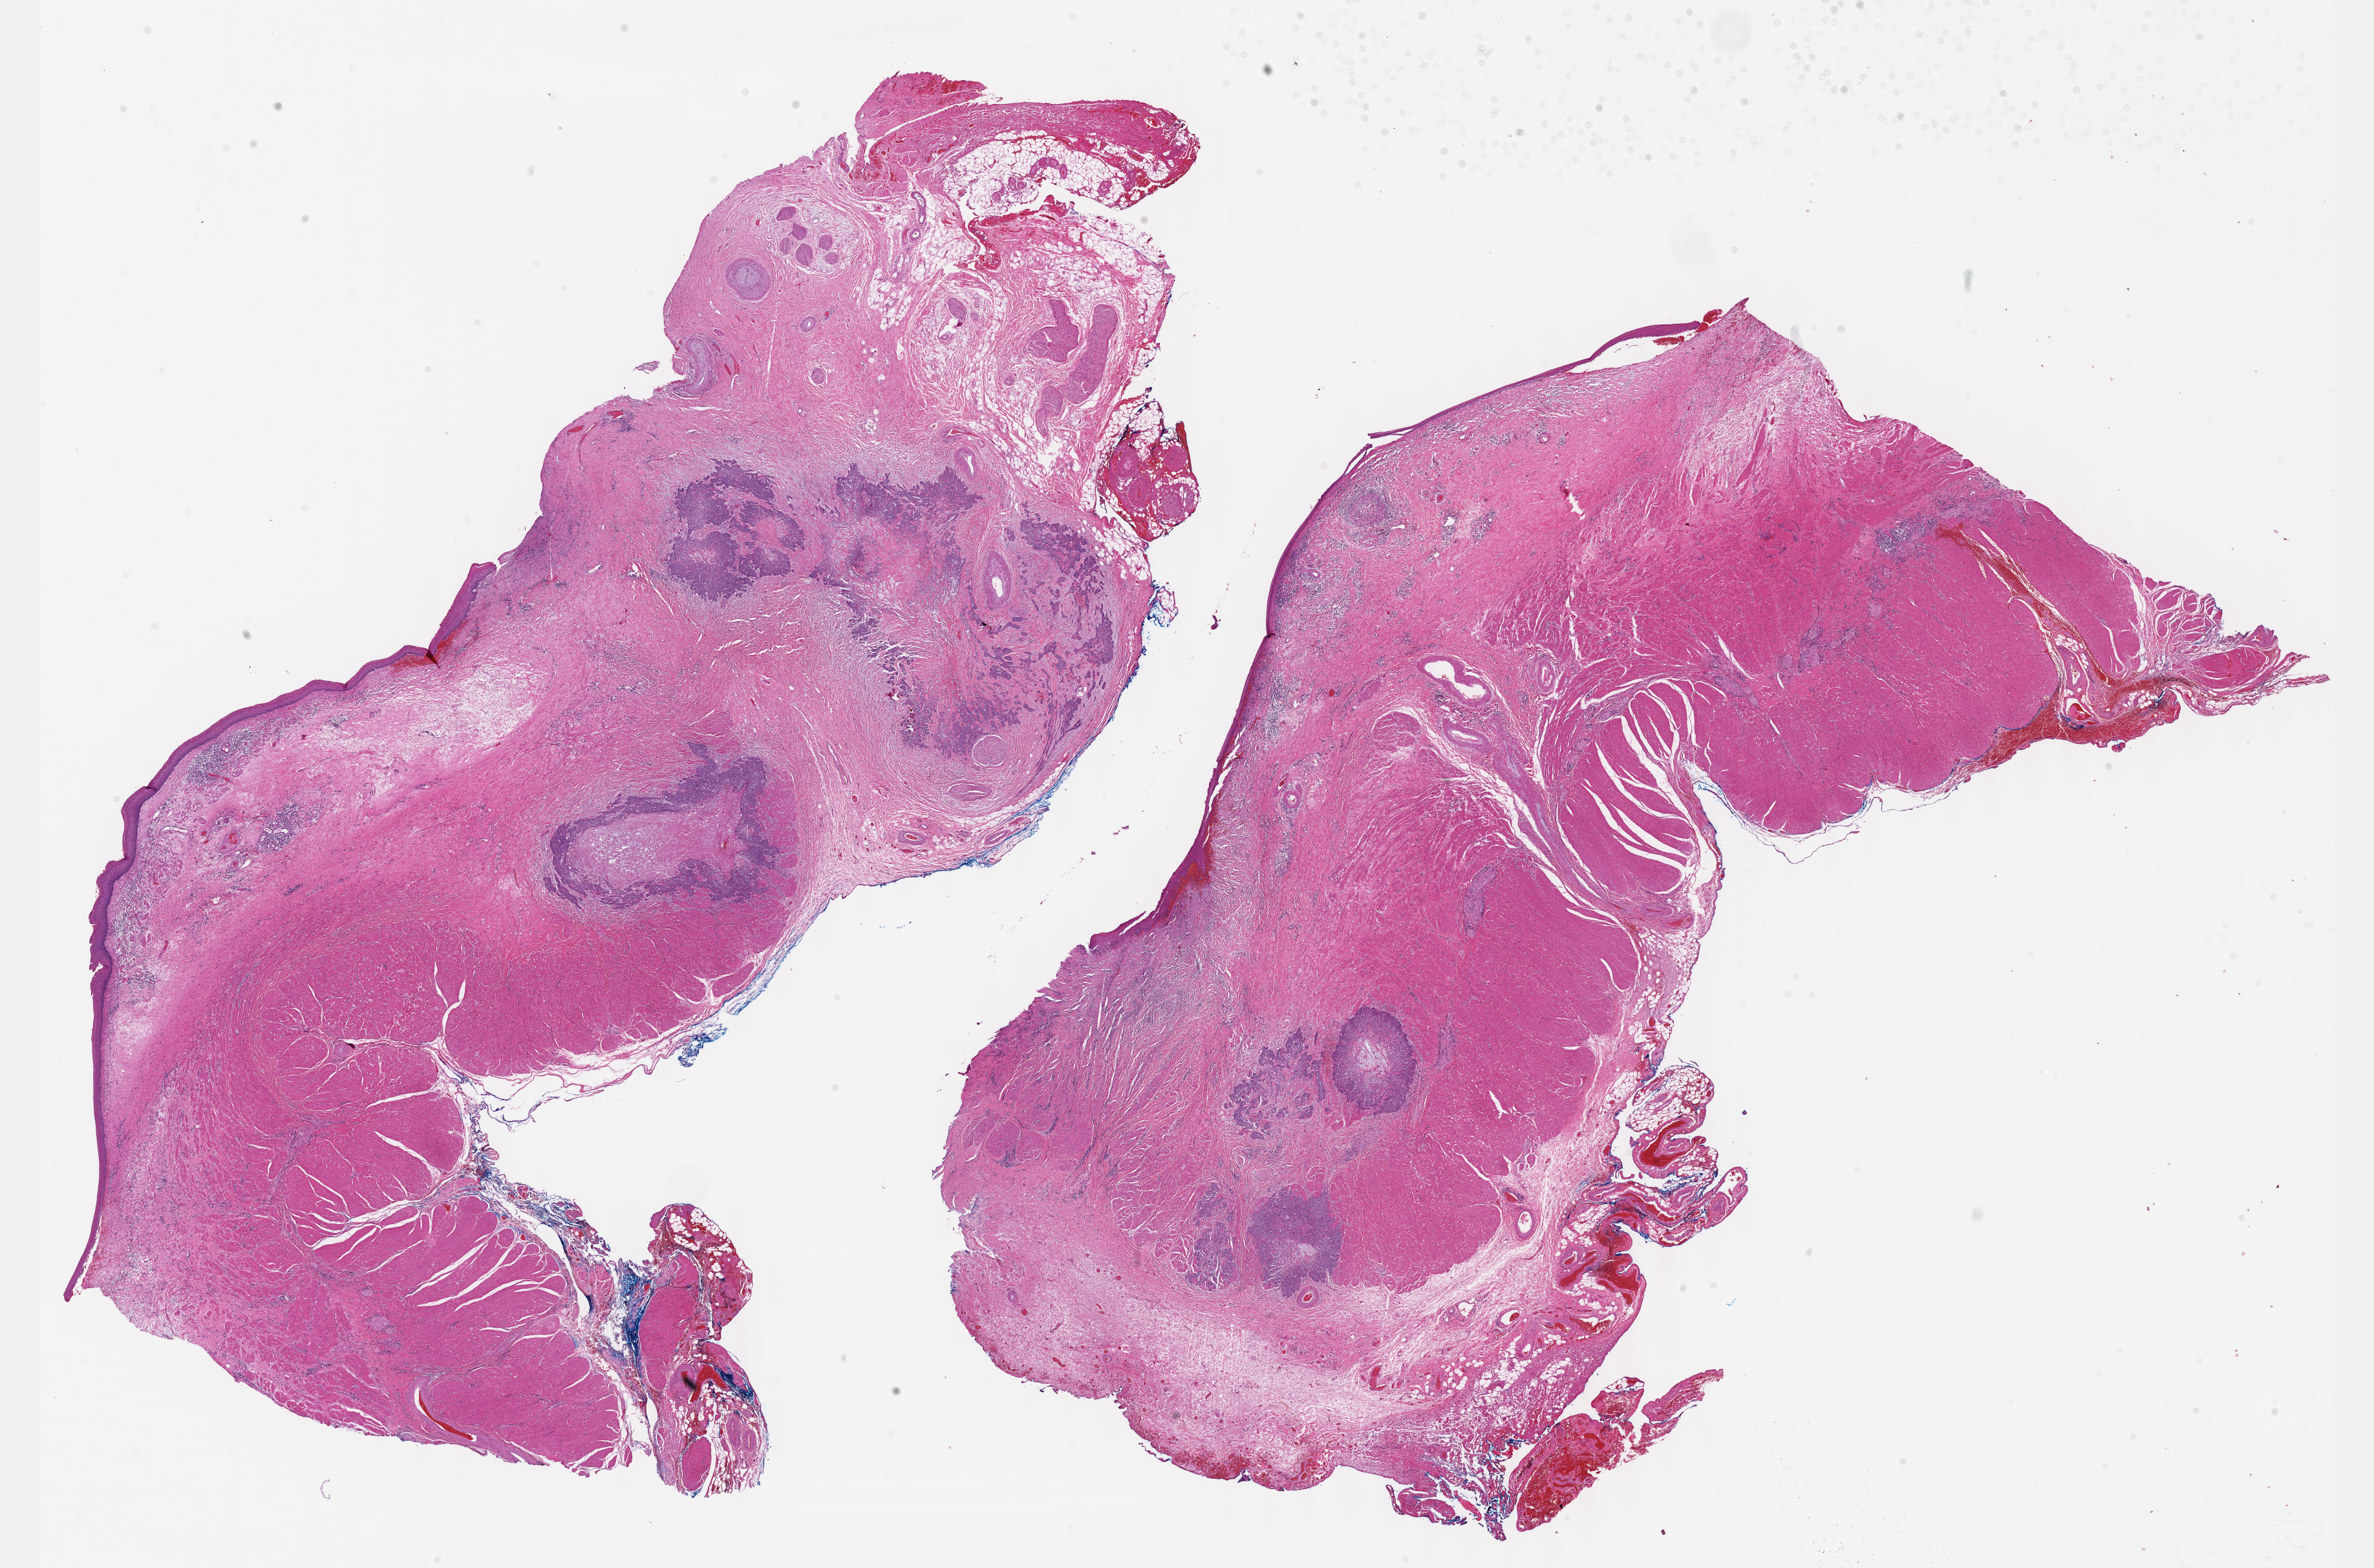
Digitized Hematoxylin and eosin (H&E) stained tissue section (whole slide), shown as a low-resolution overview of the whole scanned area (about 29.7 x 19.6 mm, from a 40x scan). Formalin-fixed paraffin-embedded (FFPE) diagnostic section. Esophagus, primary tumour sample. Patient: male, age at initial diagnosis 67 years. Histologic grade: G3 (poorly differentiated).
- histologic diagnosis: Squamous cell carcinoma, NOS
- TNM: T3 N0 MX
- AJCC pathologic stage: IIB (7th edition)